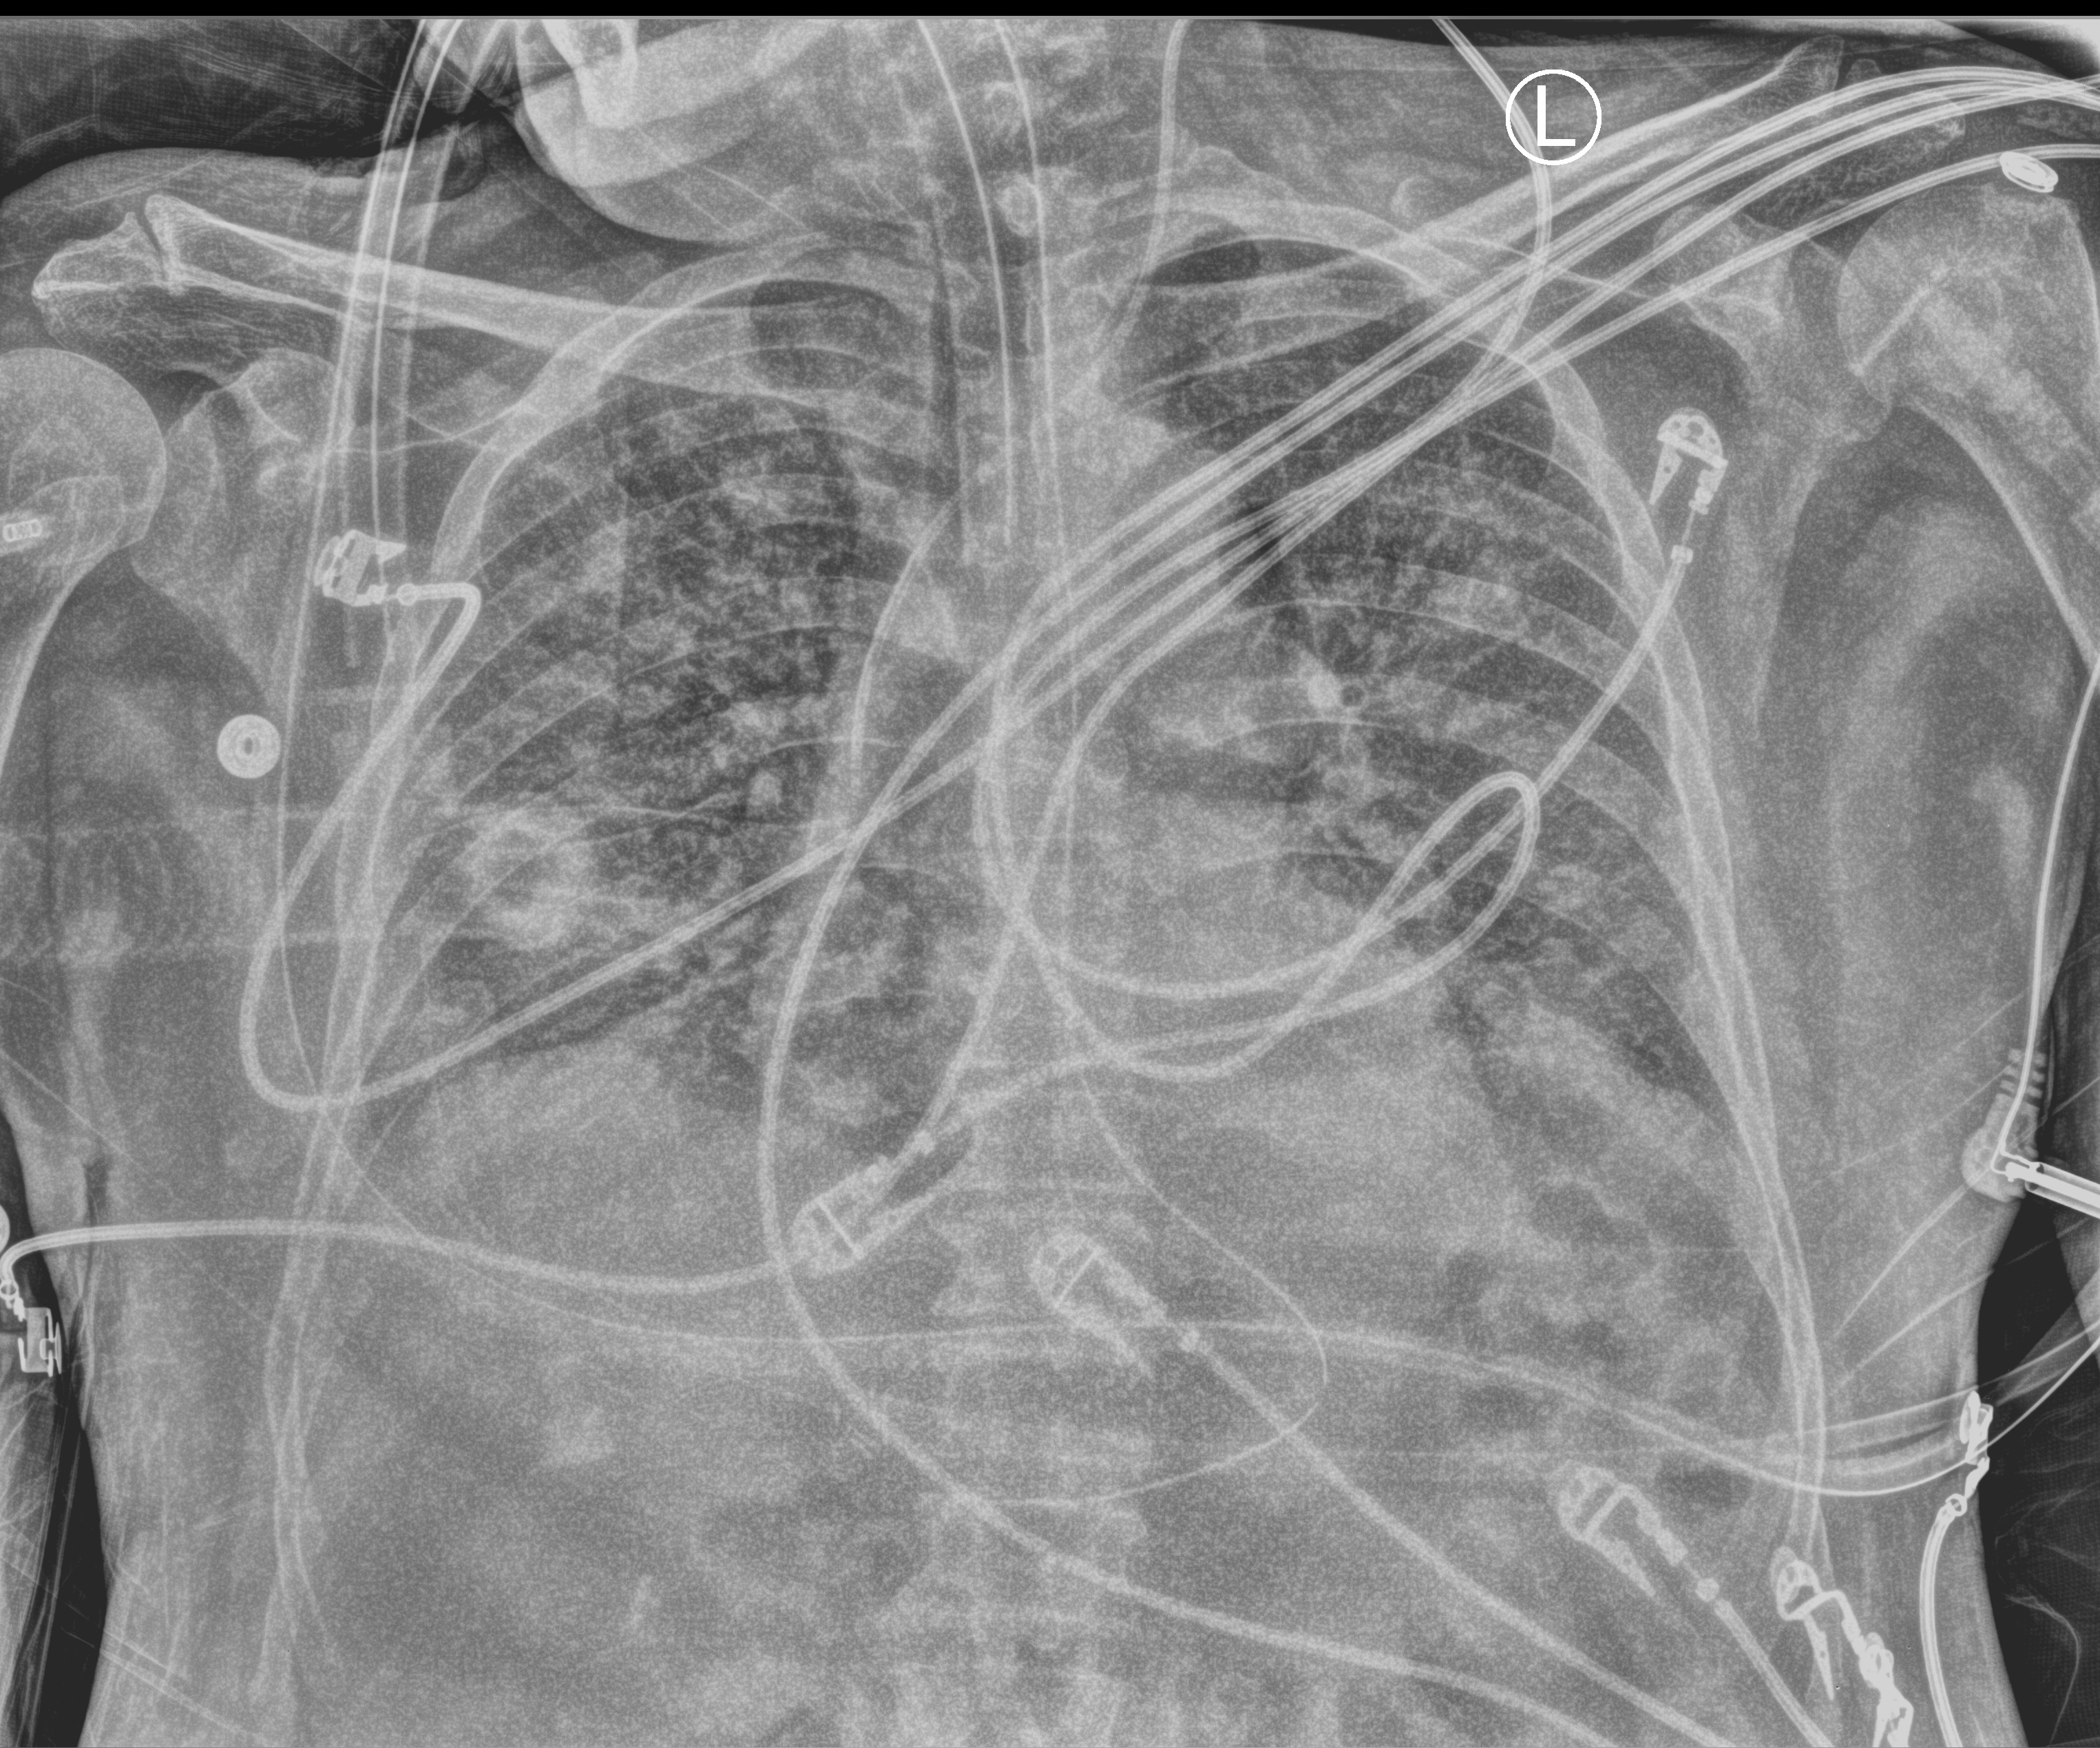
Chest X-ray (portable), anteroposterior (AP) projection. Male patient hospitalised with COVID-19, age 60–74 years.
Hospital-stay facts (about this admission, not read from this image; timing relative to this image not recorded): admitted to intensive care during this hospital stay: yes.